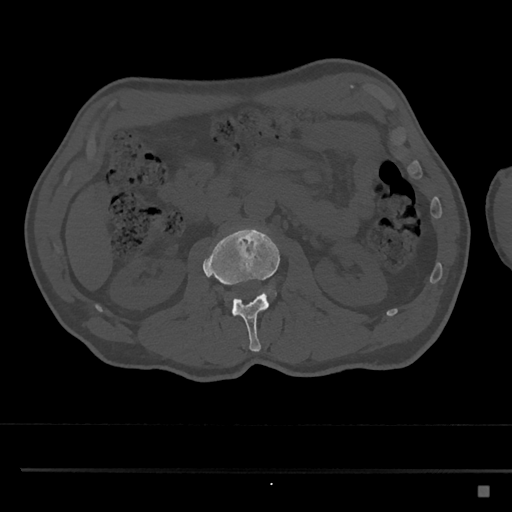
CT including the spine, one axial slice; slice 745 of 797 in the series (ordered by position); reconstruction kernel Br40s/3; bone window (W 1800 / L 400 HU); 512 × 512 image matrix, field of view 391 × 391 mm. Male patient, age 59 years. Case-level facts recorded for this patient, not image findings: primary cancer: prostate.
Annotated regions visible in this slice (semi-automatic segmentation, software-assisted and operator-edited):
- L2 vertebra: bounding box (x1, y1, x2, y2) in pixels: (202, 227, 281, 352)
- L3 vertebra: (270, 287, 276, 295)